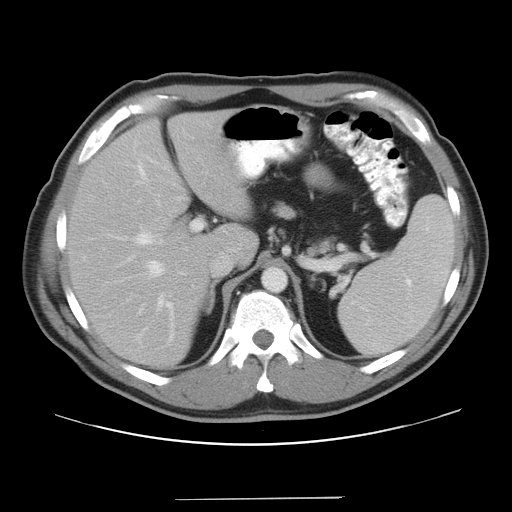
Contrast-enhanced abdominal CT, one axial slice; position 27 of 37 along the scan axis; reconstruction kernel STANDARD; 120 kVp; intravenous contrast given; soft-tissue window (W 400 / L 40 HU); 7.5 mm slice thickness; 512 × 512 image matrix, field of view 400 × 400 mm. Male patient, age 46 years. From the clinical record (not read from this slice): diagnosis: colorectal cancer liver metastases, imaged before liver resection; multiple liver metastases: yes; largest metastasis: 1 cm; disease in both lobes: no.
Structures marked on this image (manually delineated by an expert):
- hepatic veins: bounding box <139,167,166,279> (left, top, right, bottom; pixels)
- liver: <69,113,255,367>
- planned liver remnant (the part of the liver to remain after resection): <69,113,255,367>
- portal vein (with intrahepatic branches): <134,219,204,344>